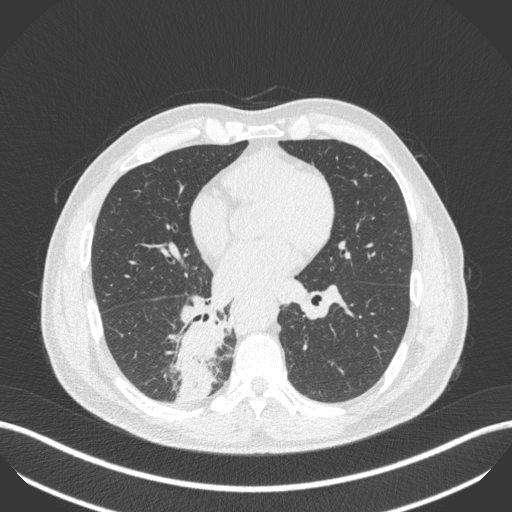
Chest CT, one axial slice; reconstruction kernel B31f; 100 kVp; lung window (W 1500 / L -600 HU); 1 mm slice thickness; 512 × 512 image matrix. Patient: male, 61 years. From the clinical record (not read from this slice): clinical TNM (as recorded): T1 N0 M0; histopathological grade: G3.
Outlined on this slice (rectangle marked by the reading radiologist):
- lung tumour (recorded histology: small cell carcinoma): box from (x=165, y=314) to (x=228, y=415) px